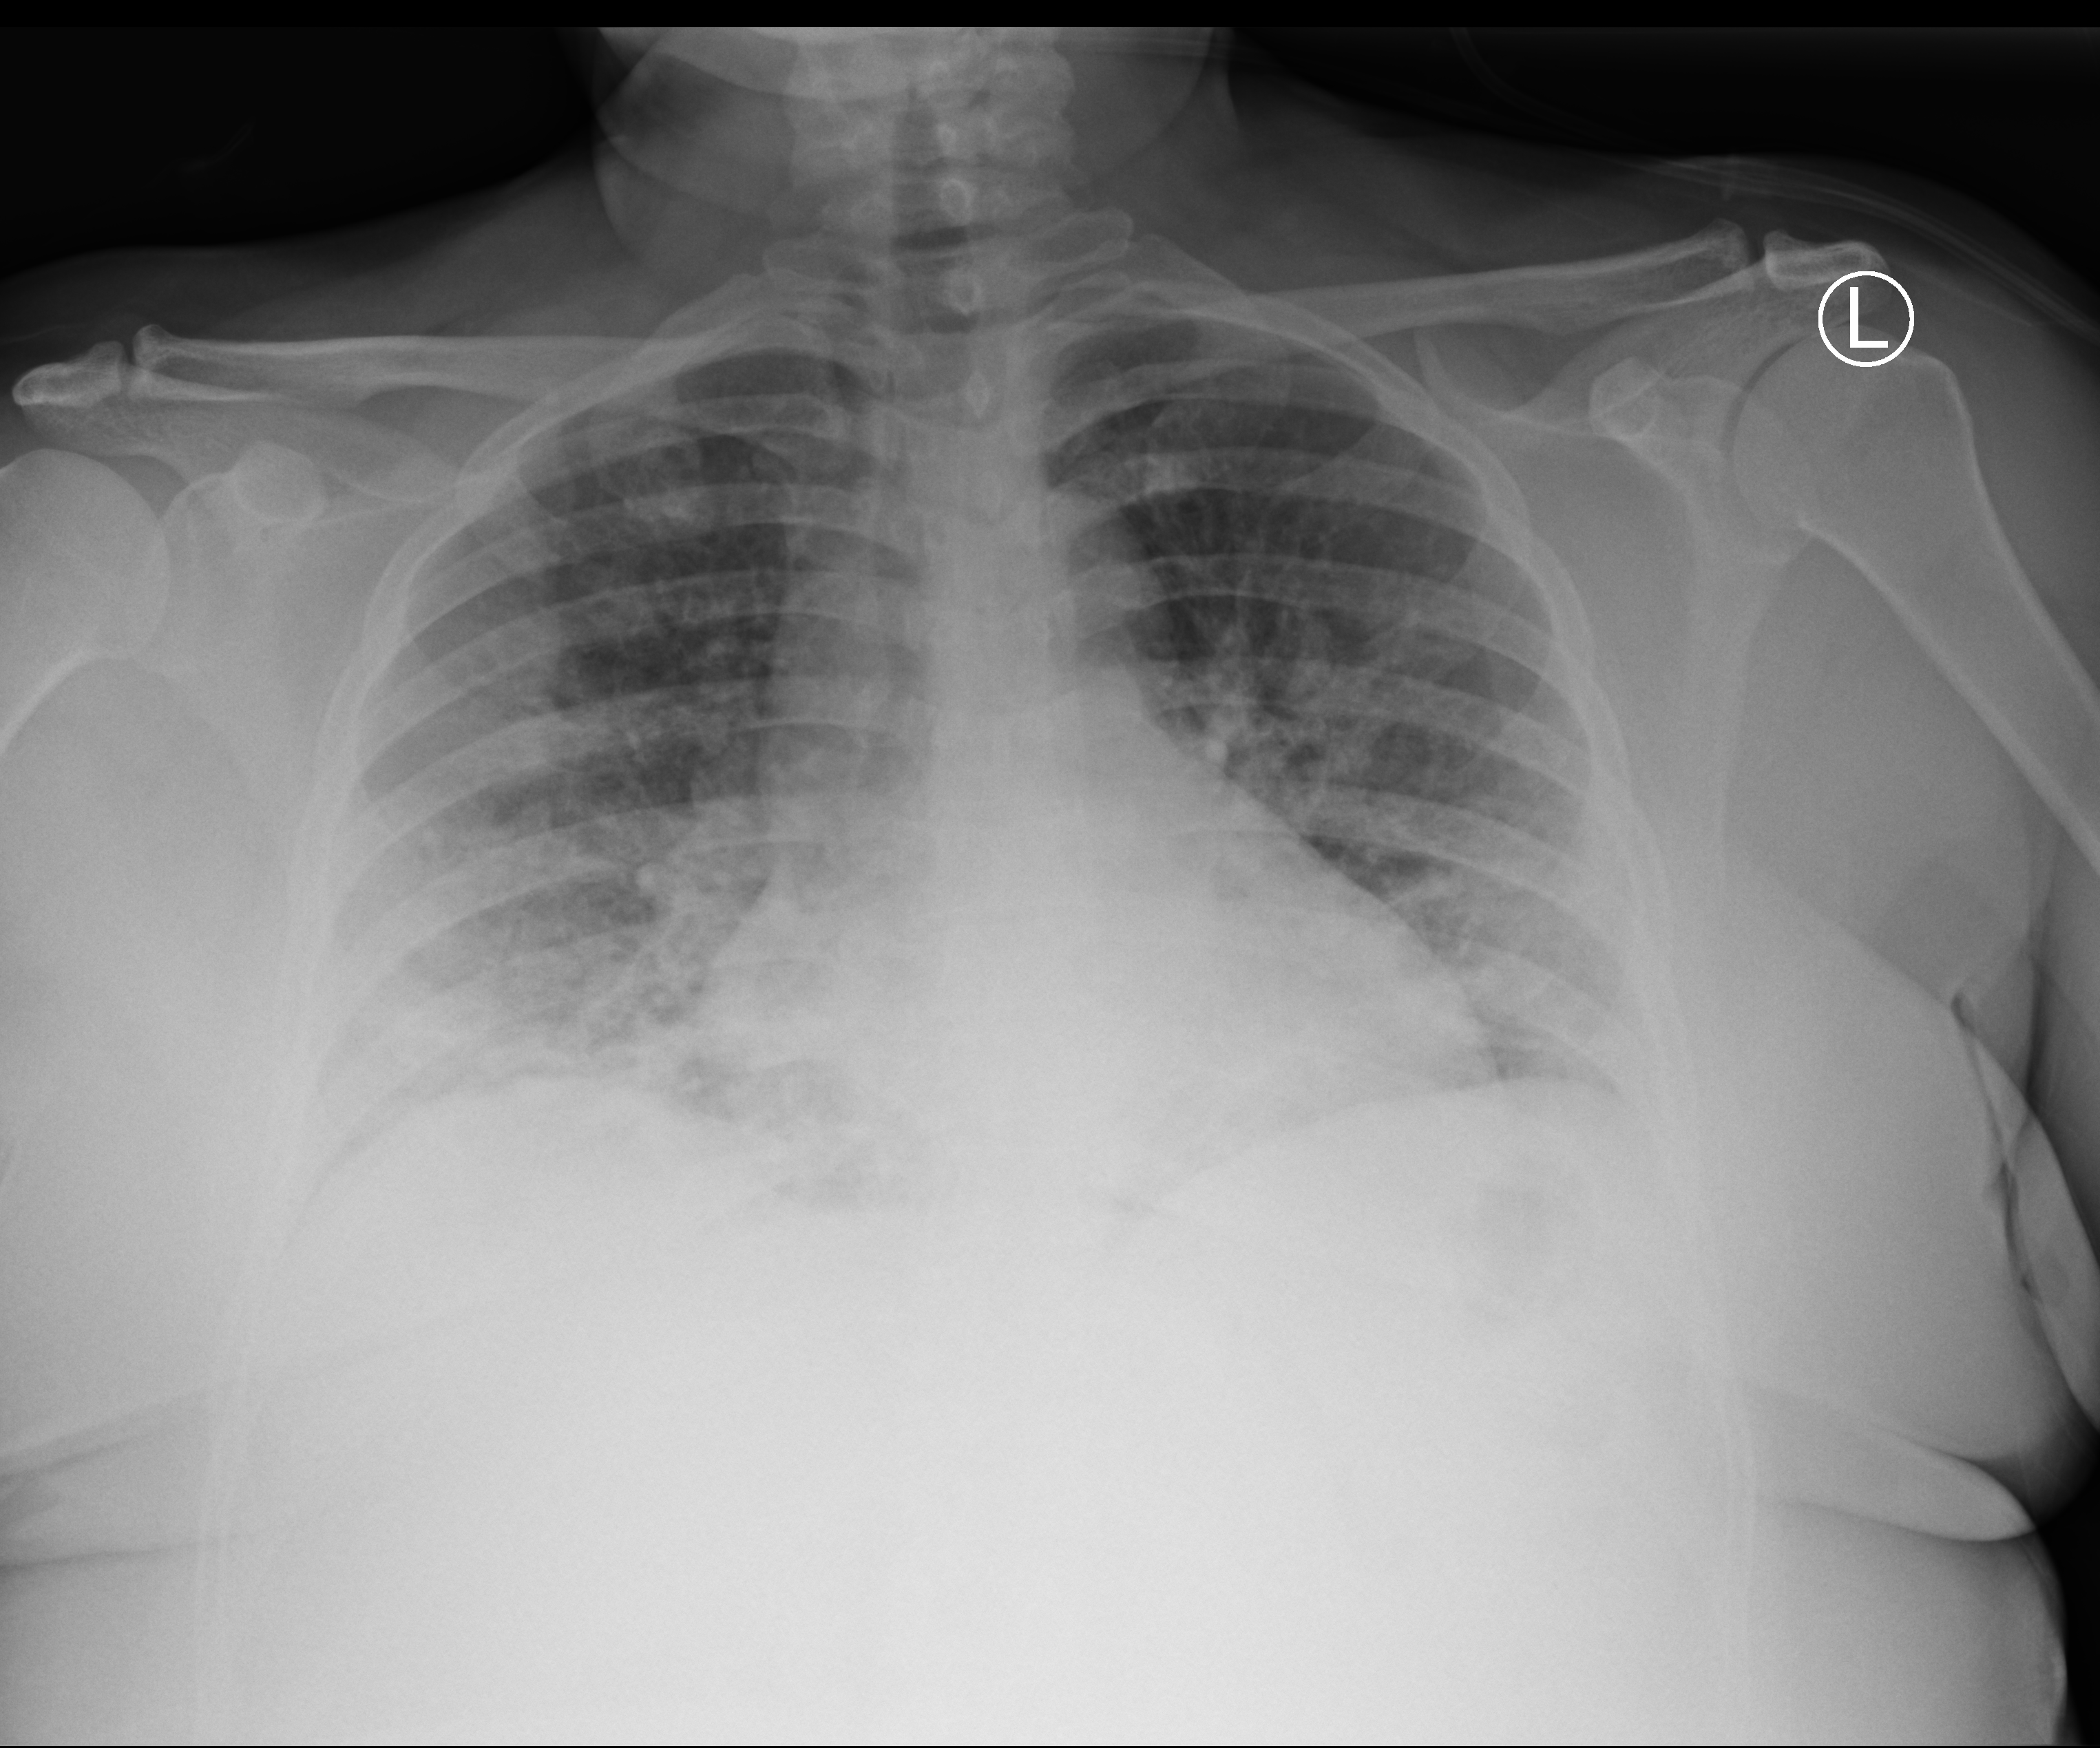
Bedside chest radiograph (computed radiography); anteroposterior (AP) projection. Patient hospitalised with COVID-19; female, aged 18–59 years.
Admission-level facts for this patient (not findings on this image; timing relative to this image not recorded): diabetes (admission record): no; other chronic lung disease (admission record): no; length of hospital stay: 6 days.